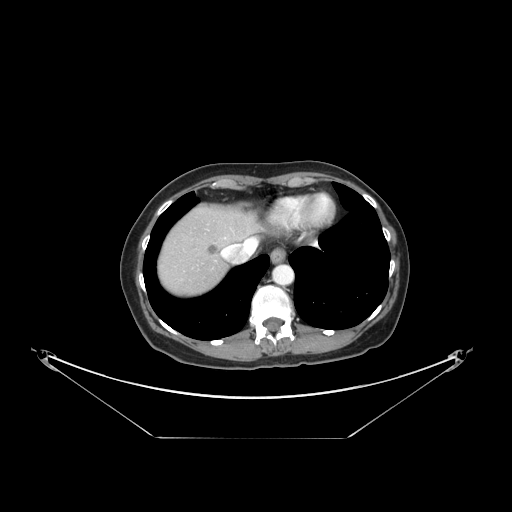
Contrast-enhanced abdominal CT, one axial slice; slice 131 of 148 in the series (ordered by position); 120 kVp; intravenous contrast given; soft-tissue window (W 400 / L 40 HU); 2.5 mm slice thickness; 512 × 512 image matrix, field of view 500 × 500 mm. Female patient, age 73 years. From the clinical record (not read from this slice): diagnosis: colorectal cancer liver metastases, imaged before liver resection; multiple liver metastases: no; largest metastasis: 1 cm; disease in both lobes: no.
Annotated regions visible in this slice (expert manual segmentation):
- liver: bounding box <158,206,255,296> (left, top, right, bottom; pixels)
- planned liver remnant (the part of the liver to remain after resection): <188,206,255,243>
- liver metastasis: <207,245,219,256>